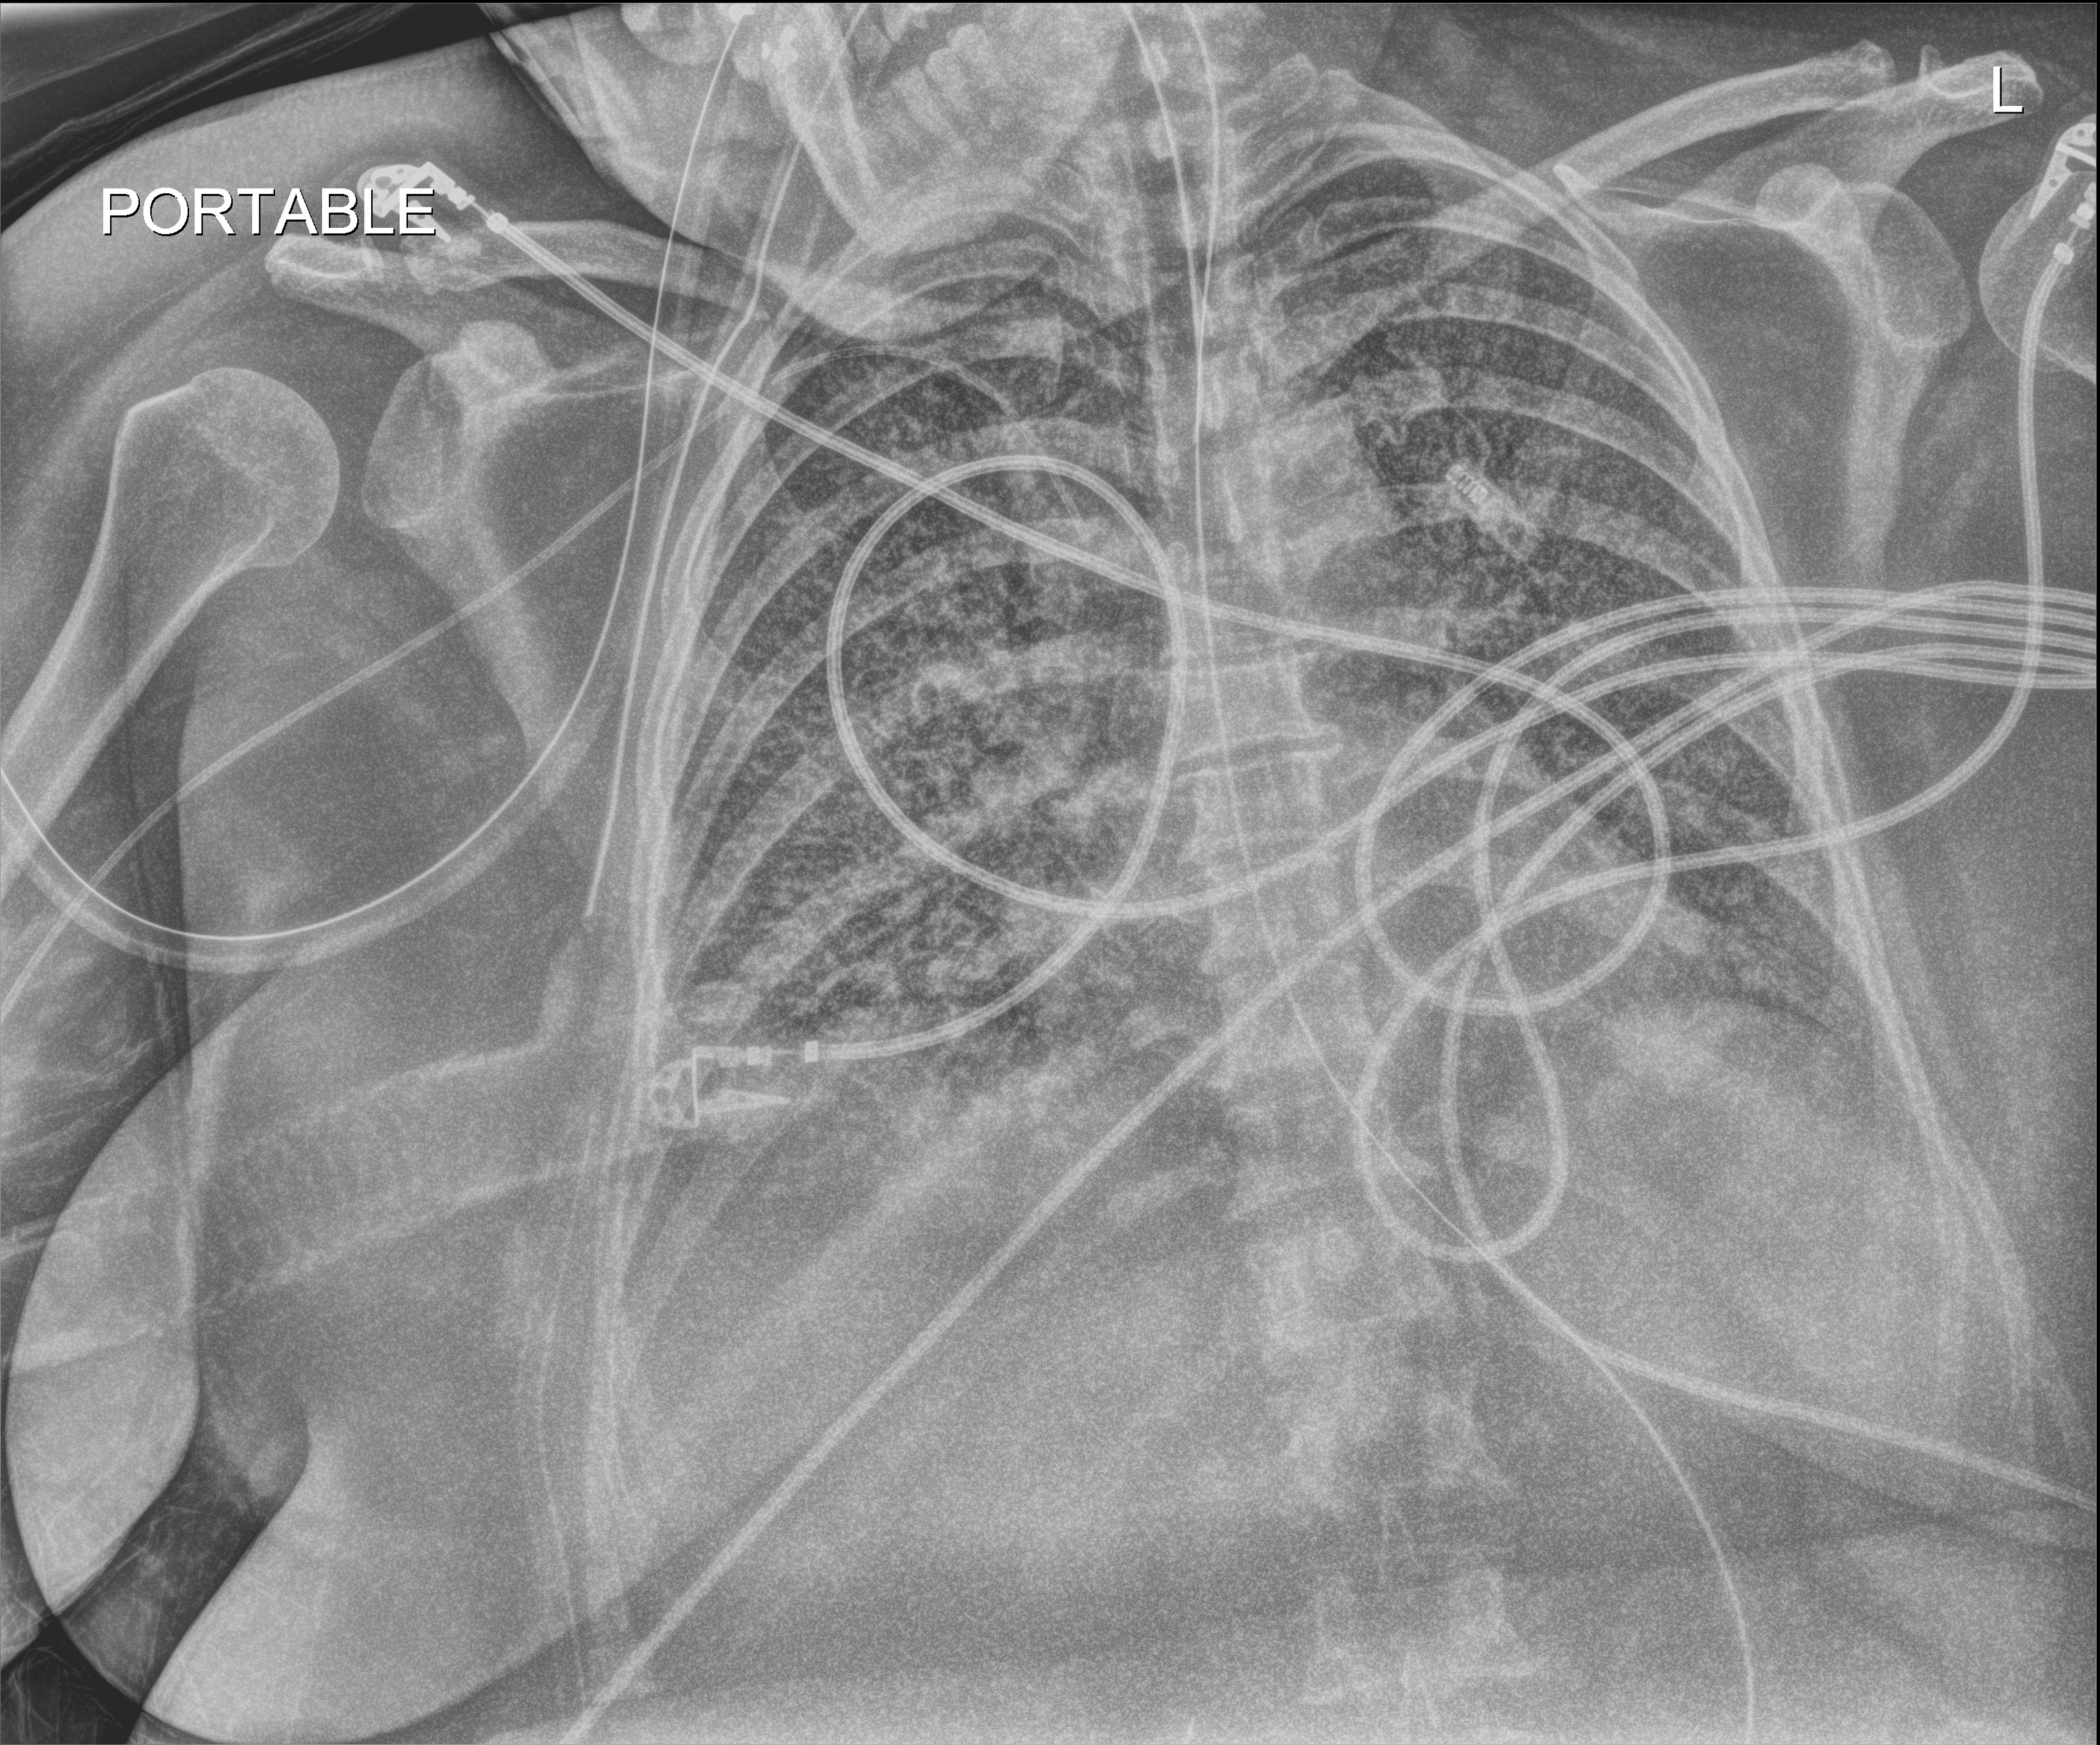
Portable chest radiograph, anteroposterior (AP) projection. Patient hospitalised with COVID-19; female, aged 18–59 years.
Hospital-stay facts (about this admission, not read from this image; timing relative to this image not recorded):
- admitted to intensive care during this hospital stay: yes
- mechanically ventilated during this hospital stay: yes
- other chronic lung disease (admission record): no